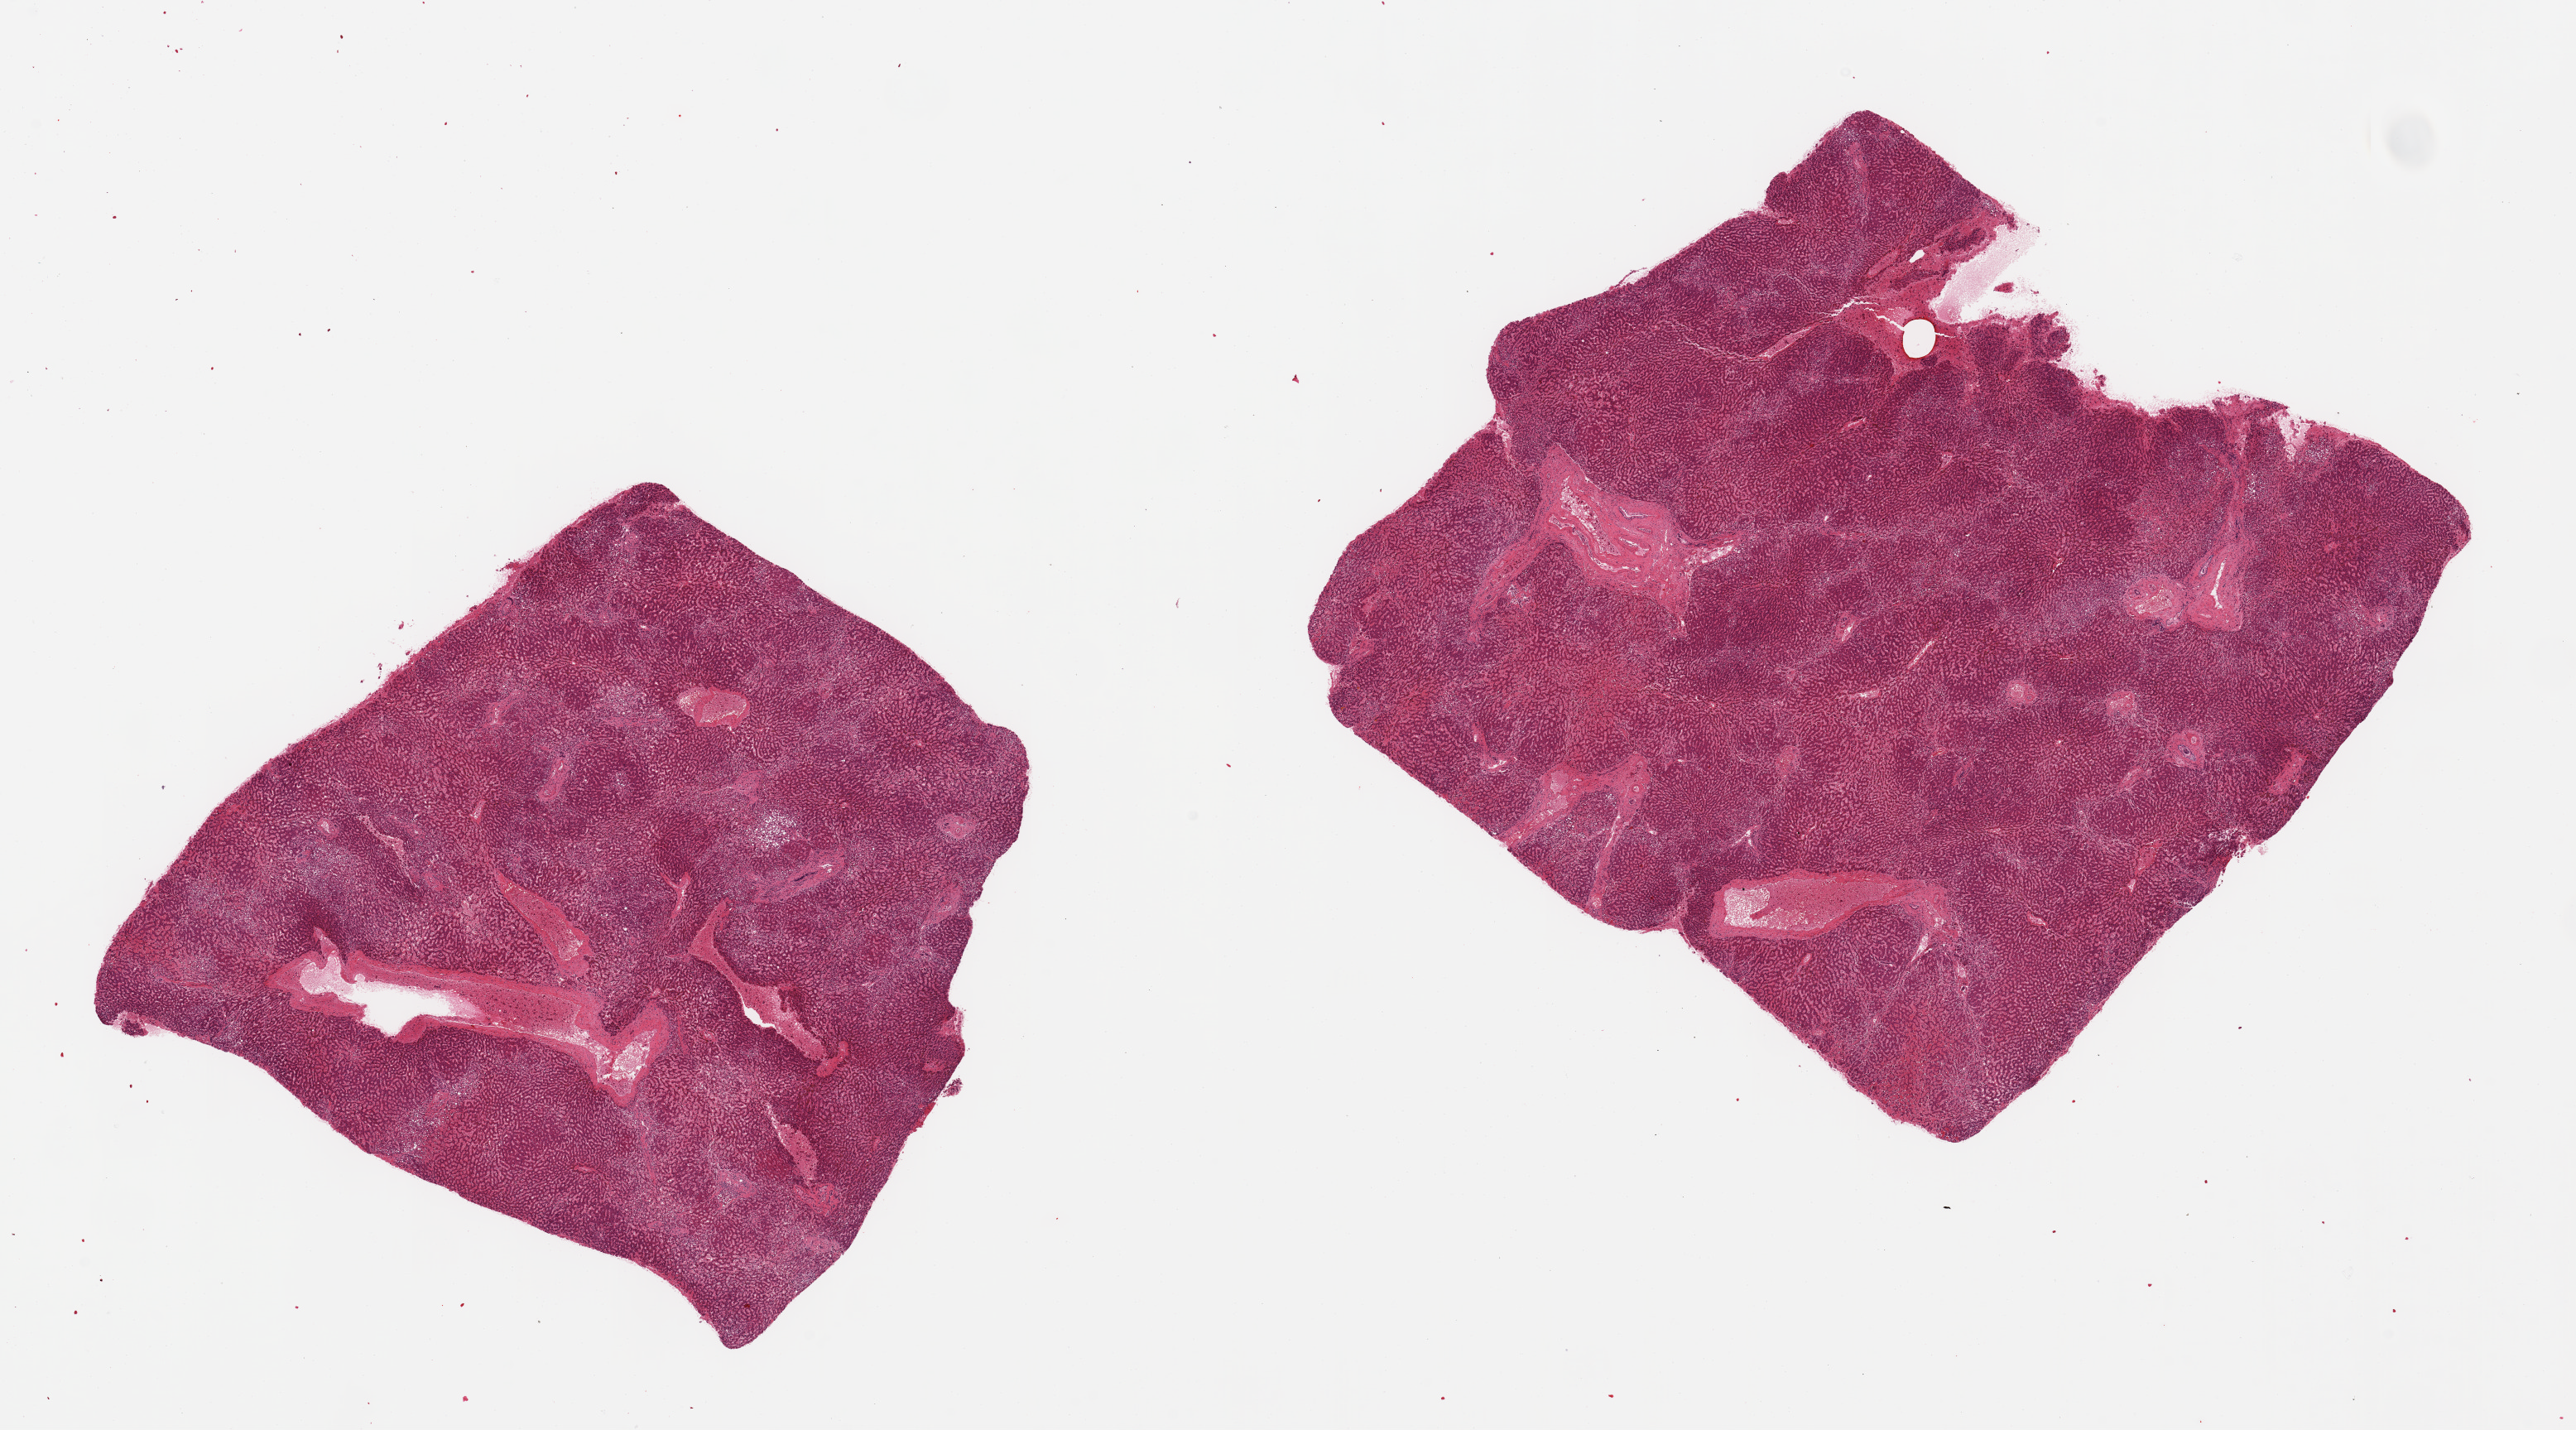
H&E whole-slide image, shown as a low-resolution overview of the whole scanned area (about 24.6 x 13.7 mm), PAXgene-fixed, paraffin-embedded tissue, sampled site (target tissue): liver, donor tissue sample. Female donor.
Review note (as recorded): 2 pieces diffuse moderate macrovesicular steatosis and moderate passive congestion.